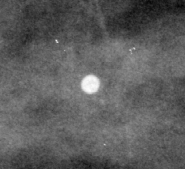
Cropped region of a digitized screen-film mammogram centred on a radiologist-marked abnormality, right breast, CC view.
- Finding: calcifications, morphology round and regular; BI-RADS assessment category 2; subtlety rating 4 on a 1 (subtle) to 5 (obvious) scale; benign without callback (not worked up further).